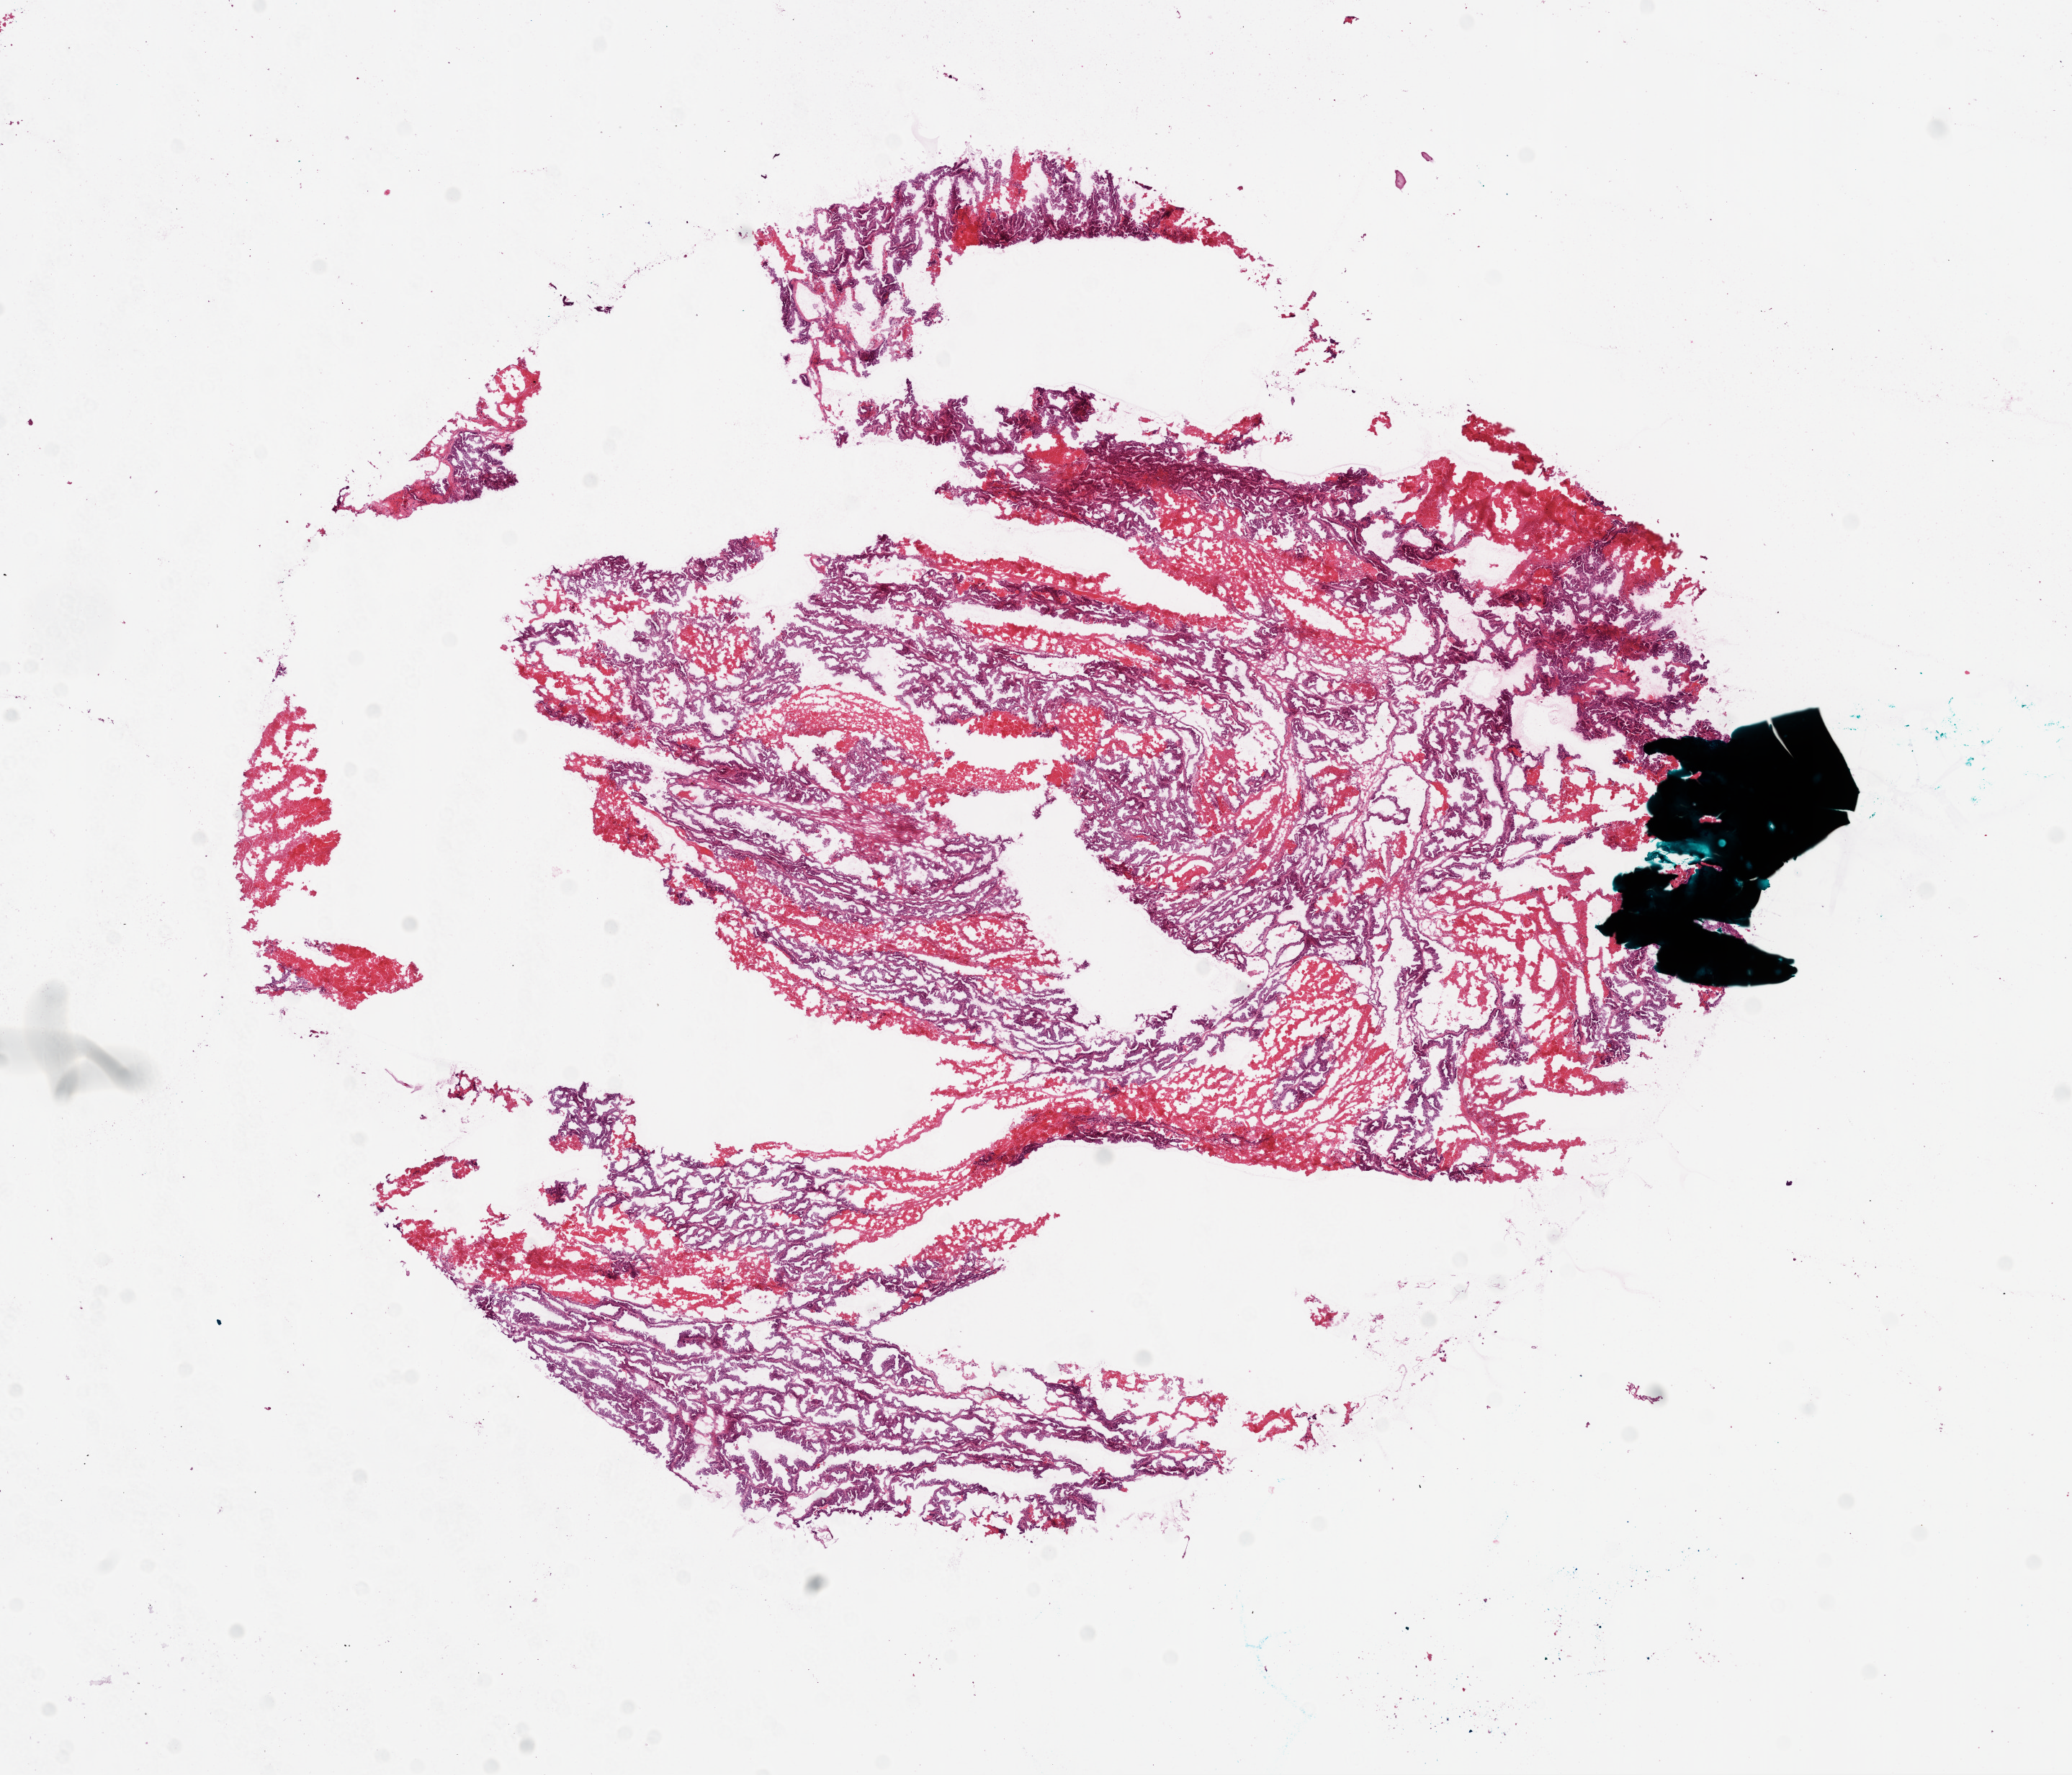
Digitized H&E-stained tissue section (whole slide), a low-resolution overview of the entire scanned area, about 11.6 x 9.9 mm (from a 20x scan), frozen section from the bottom of the tissue portion, sample: primary tumour, ovary. Female, age 73 years at initial diagnosis. Histologic grade: G3 (poorly differentiated). Composition of this section per pathologist review: tumour cells 70%, tumour nuclei 85%, normal cells 10%, stromal cells 5%, necrosis 15%.
Laterality: right. Pathologic diagnosis: Serous cystadenocarcinoma, NOS. FIGO stage: IV.